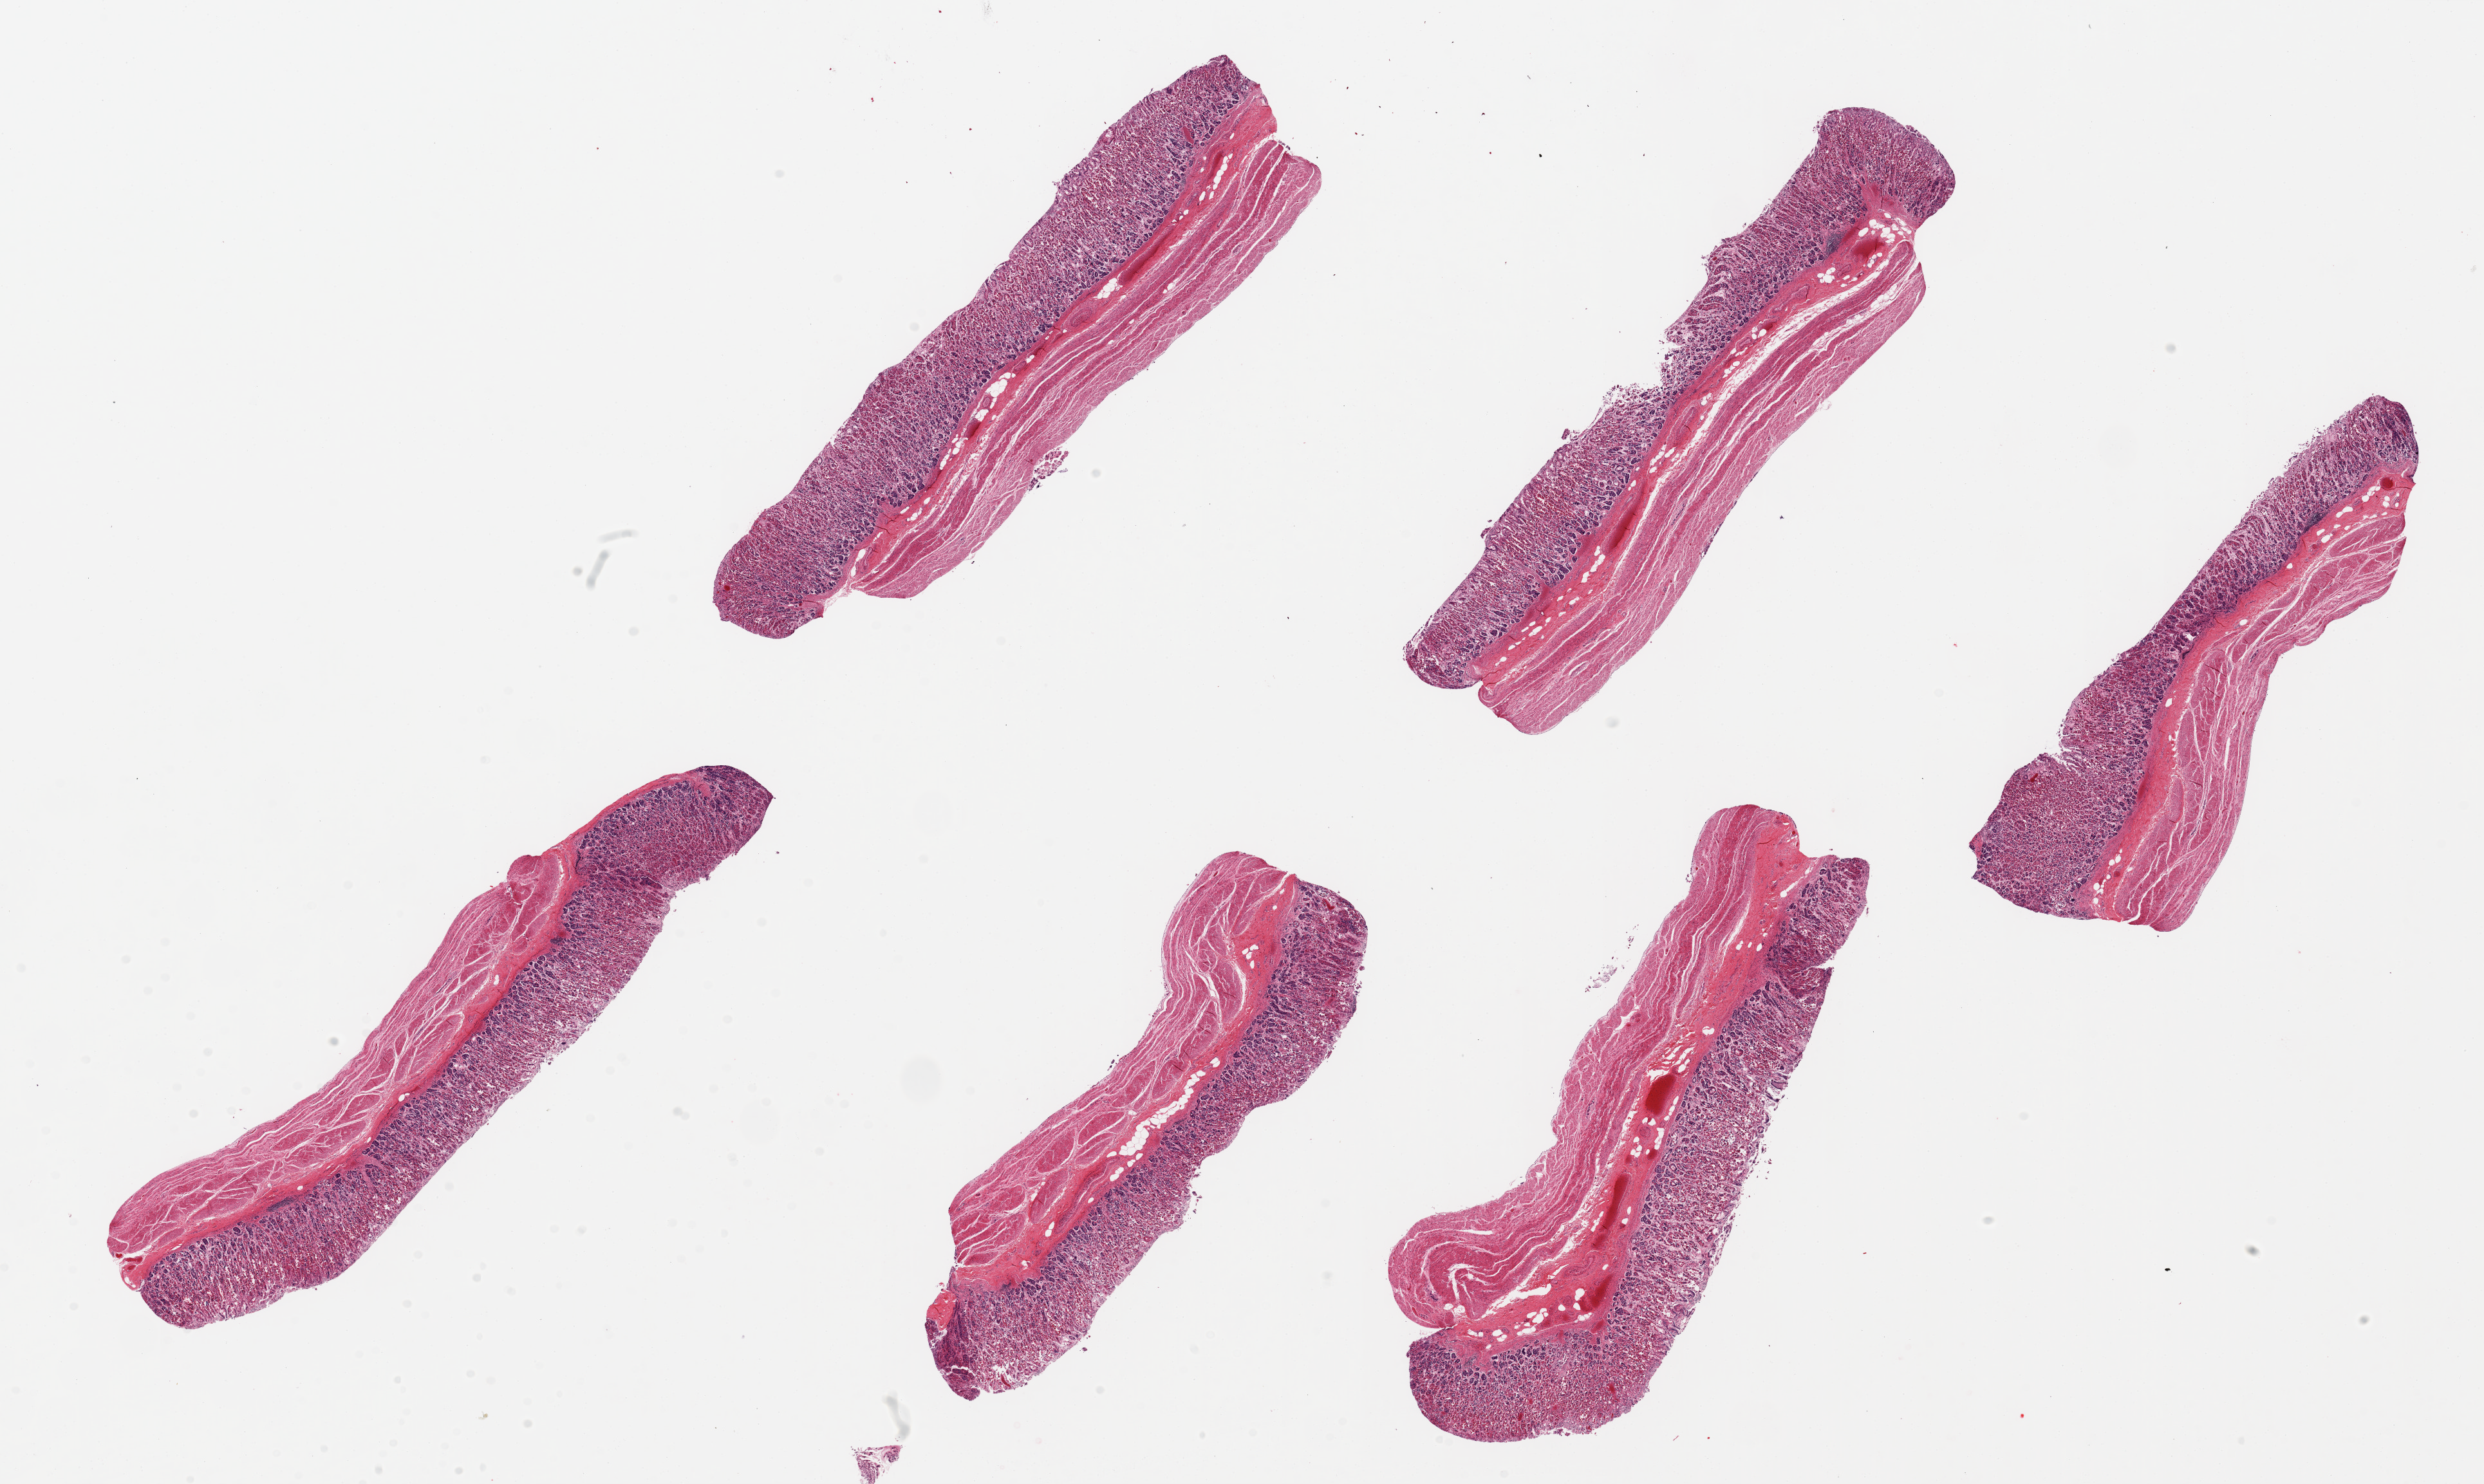
H&E whole-slide image — a low-resolution overview of the entire scanned area, about 30.5 x 18.2 mm (slide scanned at 20x); PAXgene-fixed paraffin-embedded (PFPE) section; section of stomach (target tissue); donor tissue sample. Donor sex: female.
Review note (as recorded): 6 pieces ~9x2.5mm; mucosa moderately-badly autolyzed, ~40-50% thickness.